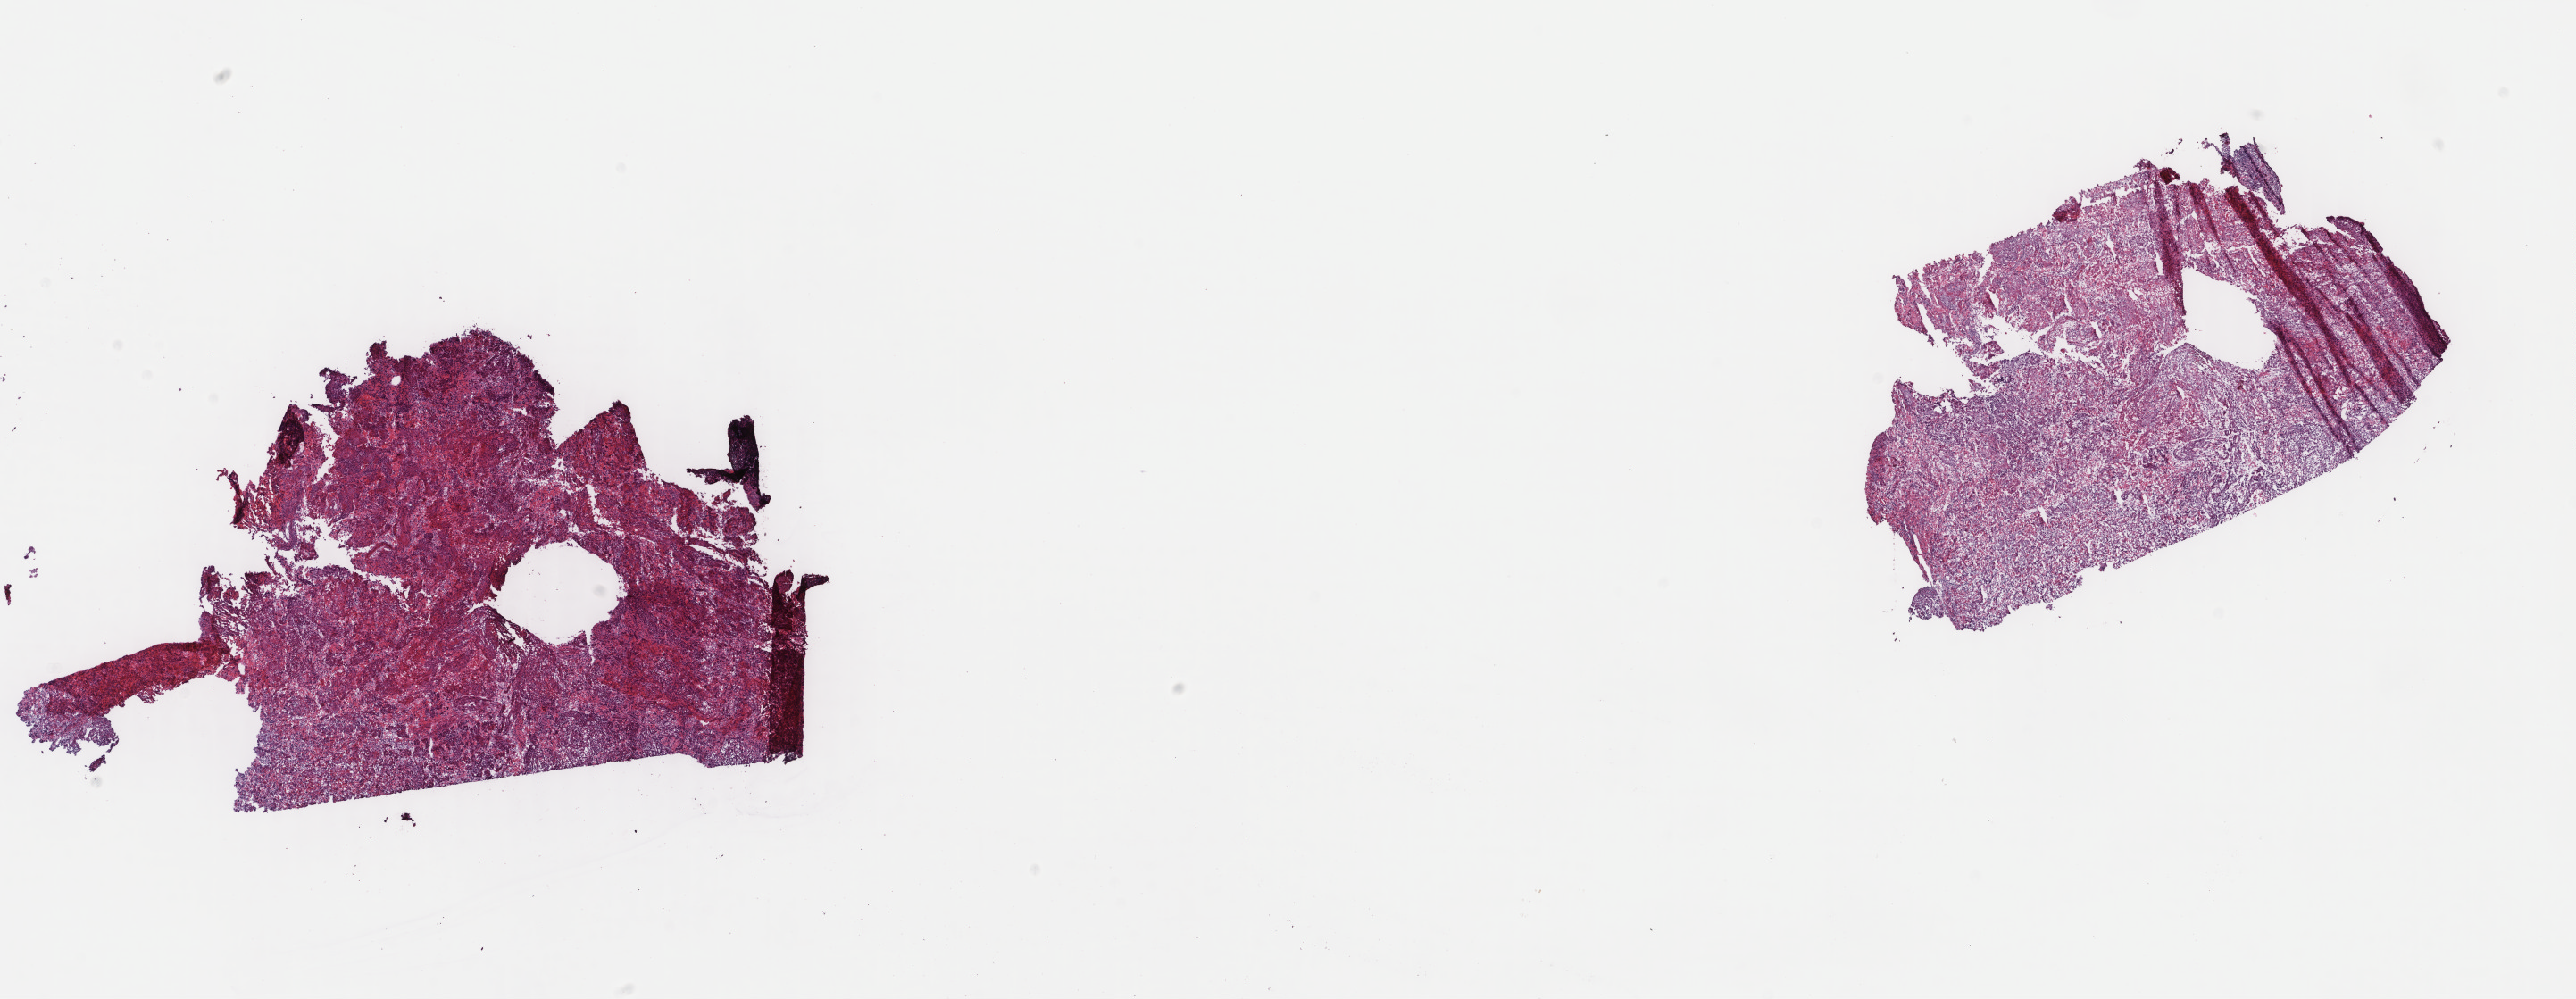
Digitized H&E-stained tissue section (whole slide), shown as a low-resolution overview of the whole scanned area (about 22.9 x 8.9 mm), frozen section from the top of the tissue portion, sample: primary tumour, cervix. Female, age 78 years at initial diagnosis. Histologic grade: G2 (moderately differentiated). Slide review estimates, as recorded: tumour cells 80%, tumour nuclei 80%, normal cells 0%, stromal cells 10%, necrosis 10%. Inflammatory infiltration, as recorded: lymphocyte infiltration 50%, monocyte infiltration 20%, neutrophil infiltration 20%.
• diagnosis: Squamous cell carcinoma, NOS (cervix uteri)
• FIGO stage: IB